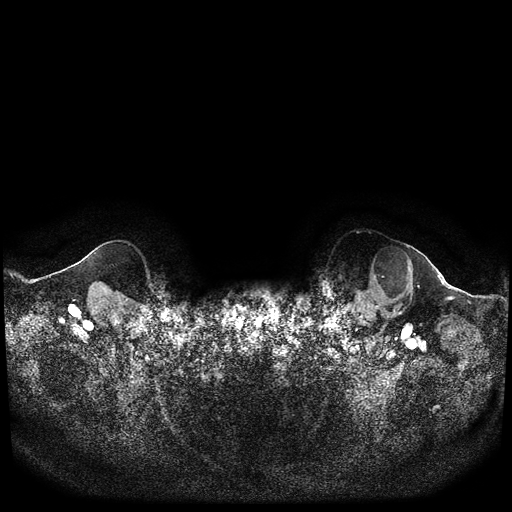
Breast MRI (dynamic contrast-enhanced, multi-phase), one axial slice; slice 104 of 116 in the series (ordered by position); dynamic contrast-enhanced series, time point 2 of 5 at this slice position (early post-contrast); 1.5 T; TE 2.6 ms, TR 5.3 ms; 2 mm slice thickness; 512 × 512 image matrix. Female patient, age 64 years.
Outlined on this slice (semi-automatically segmented with operator editing):
- breast lesion (labelled 'tumour' in the annotation; benign lesions carry a separate 'benign' label): bounding box <358,245,414,313> (left, top, right, bottom; pixels)